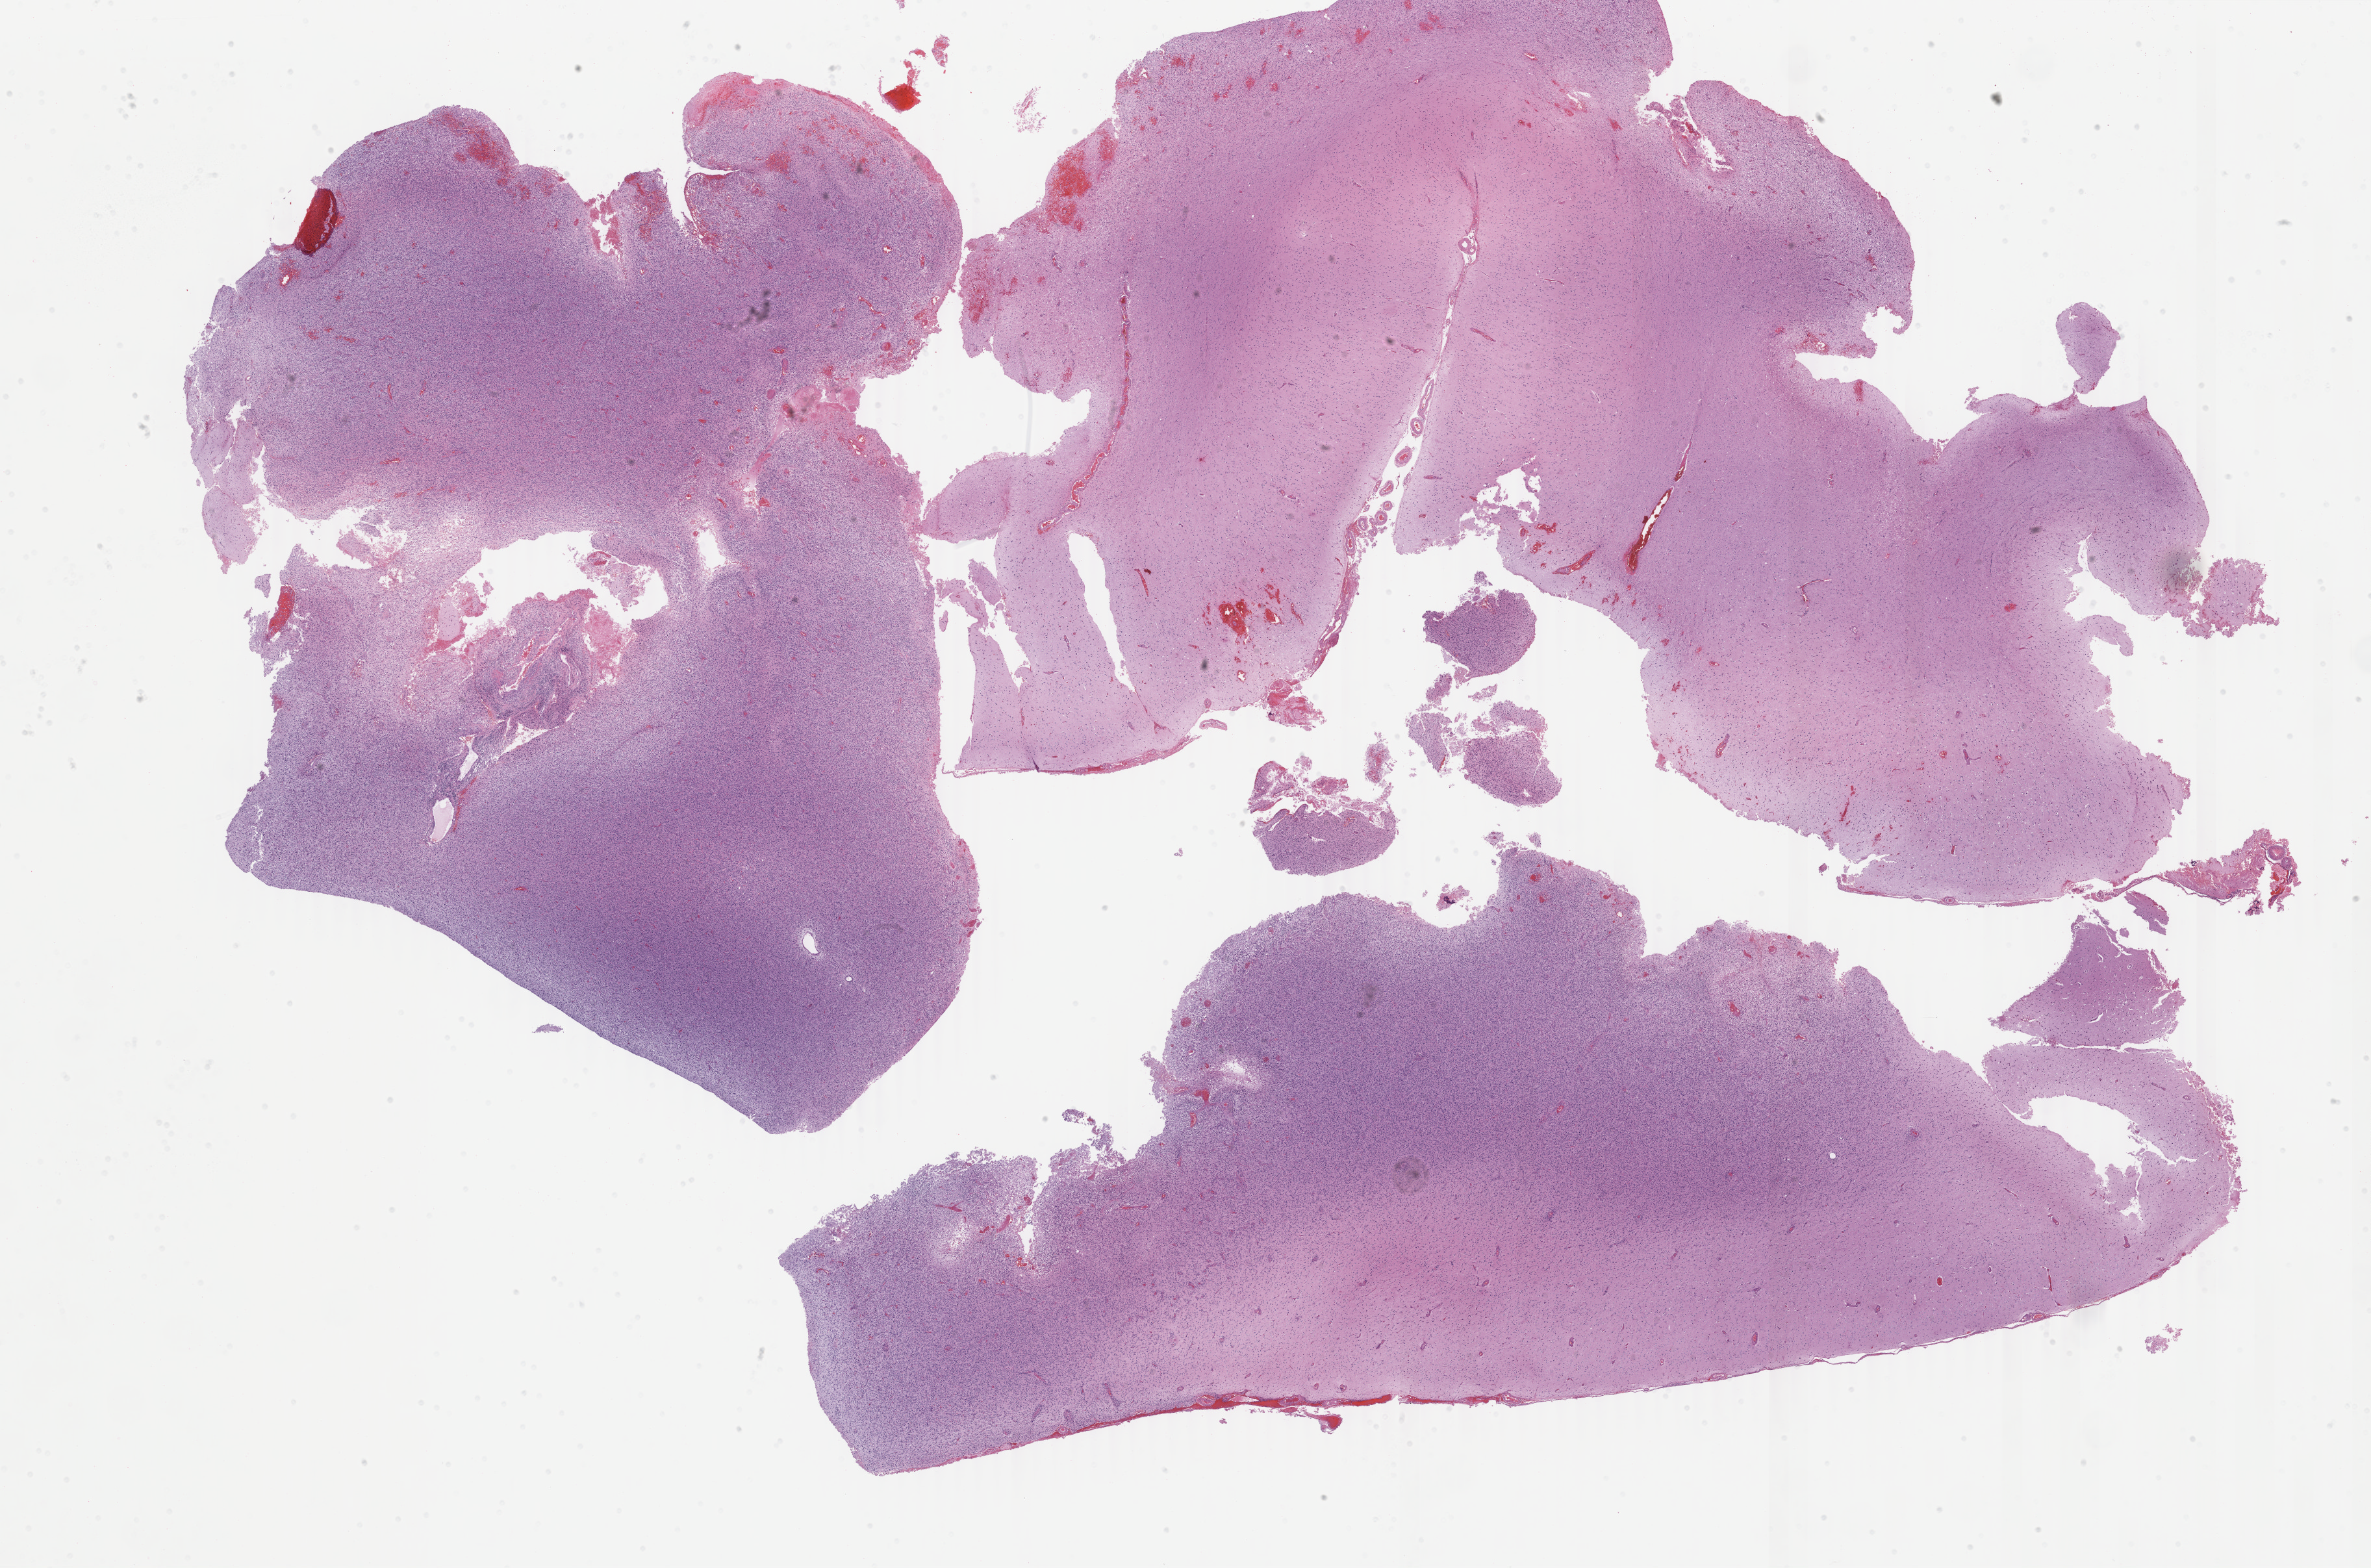
Whole-slide histology image, Hematoxylin and eosin (H&E) stained, whole scanned area (about 29.0 x 19.2 mm, slide scanned at 40x) shown as a low-resolution overview, formalin-fixed paraffin-embedded (FFPE) diagnostic section, brain, primary tumour sample. Male patient; age at initial diagnosis 68 years.
Pathologic diagnosis: Glioblastoma.